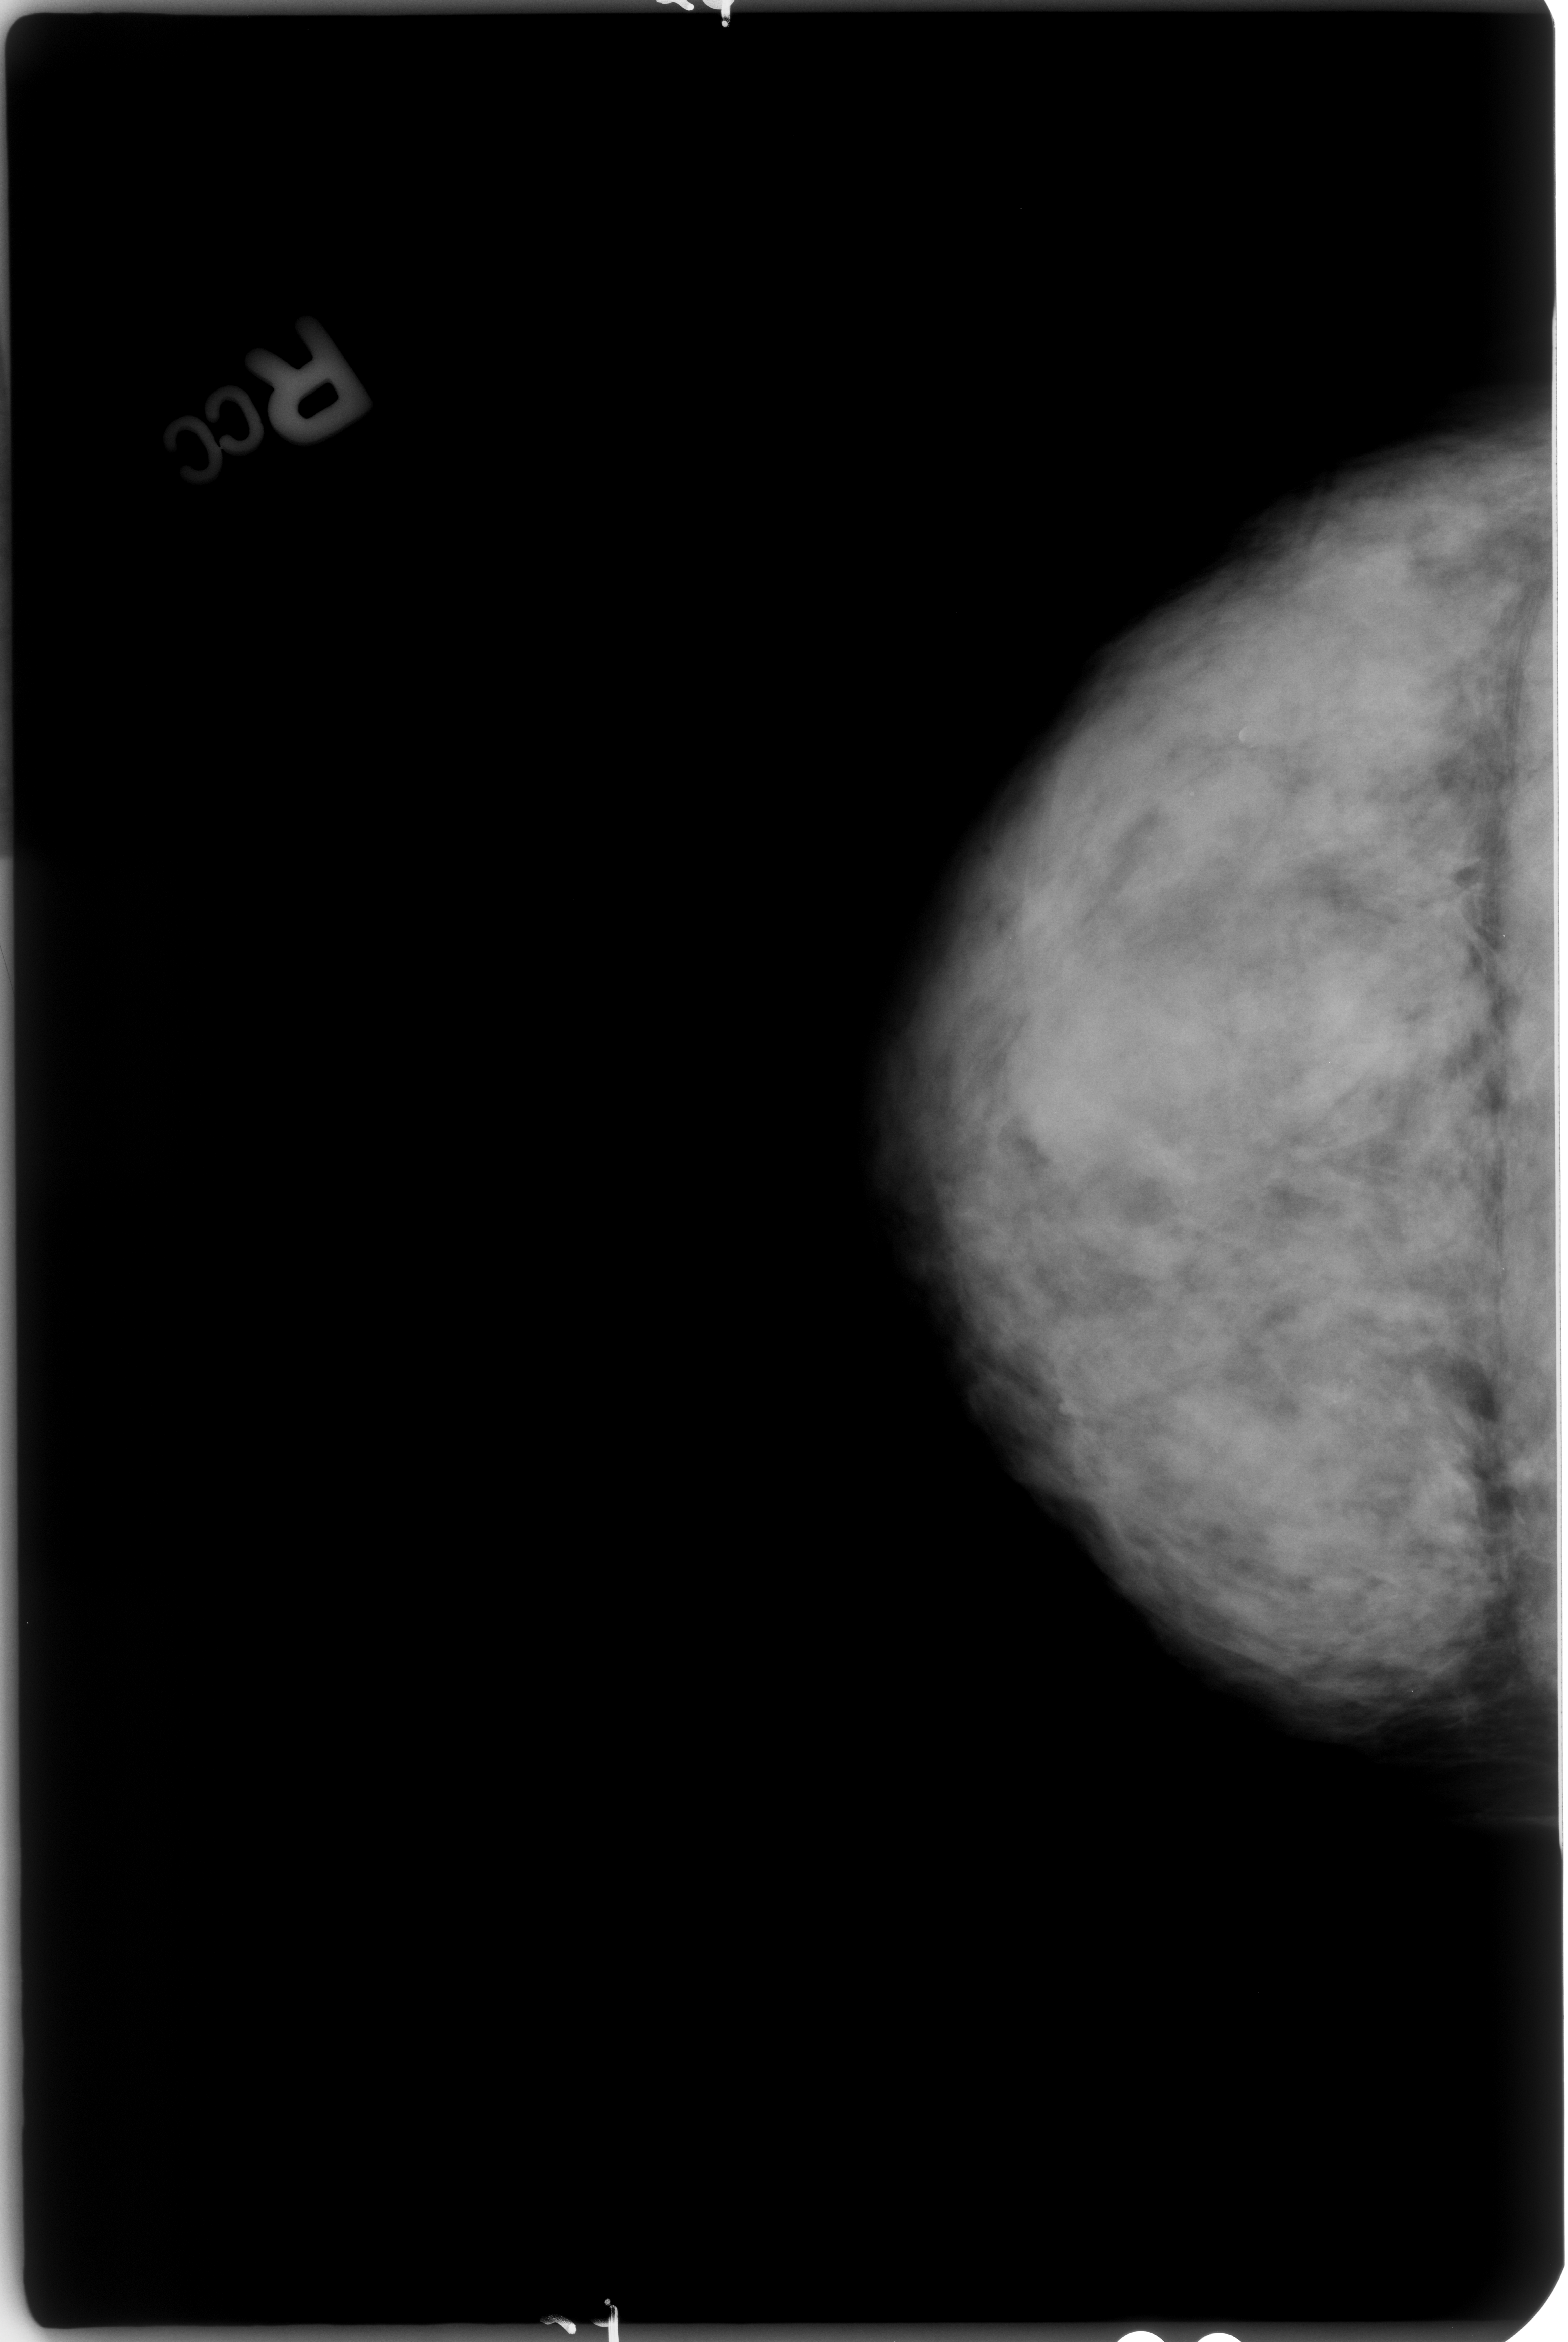
Scanned film-screen mammogram. Right breast. Craniocaudal (CC) view. Breast composition: extremely dense (BI-RADS density category 4 of 4). 1568 × 2342 image matrix.
Expert-marked regions of interest on this film, with their recorded descriptors:
- calcifications, morphology lucent center; BI-RADS assessment category 2; benign; no additional work-up was recommended (outcome (as recorded, no biopsy): benign without callback): bounding box (x1, y1, x2, y2) in pixels: (1233, 721, 1259, 759)